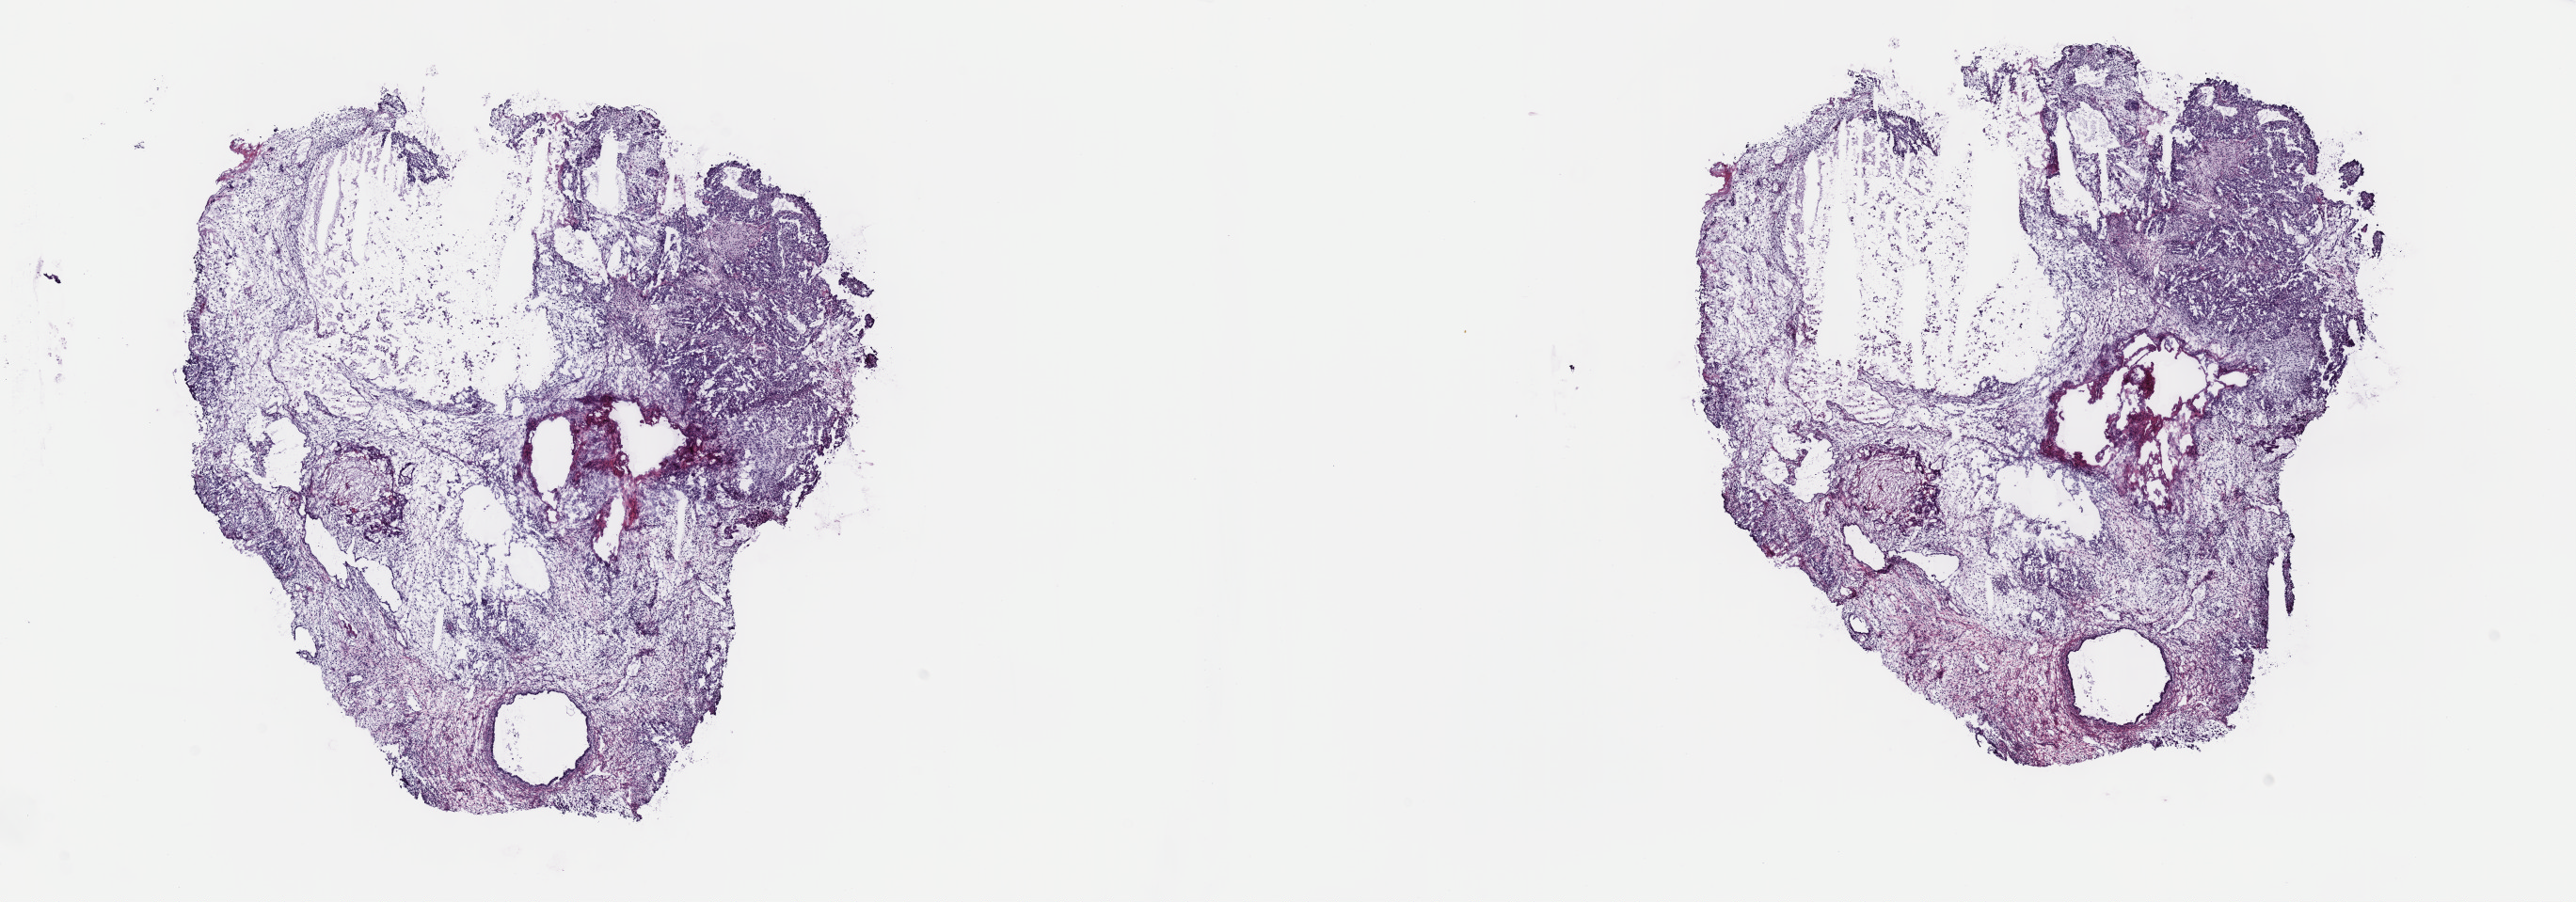
Whole-slide histology image, Hematoxylin and eosin (H&E) stained — low-resolution overview of the scanned area, about 22.1 x 7.8 mm (from a 40x scan); frozen section from the top of the tissue portion; sample: primary tumour, testis. Patient: male, age at initial diagnosis 22 years. Slide review estimates, as recorded: tumour cells 100%, tumour nuclei 70%, normal cells 0%, stromal cells 0%, necrosis 0%. Inflammatory infiltration, as recorded: lymphocyte infiltration 3%, monocyte infiltration 0%, neutrophil infiltration 0%.
AJCC pathologic stage: I. Histologic diagnosis: Embryonal carcinoma, NOS.